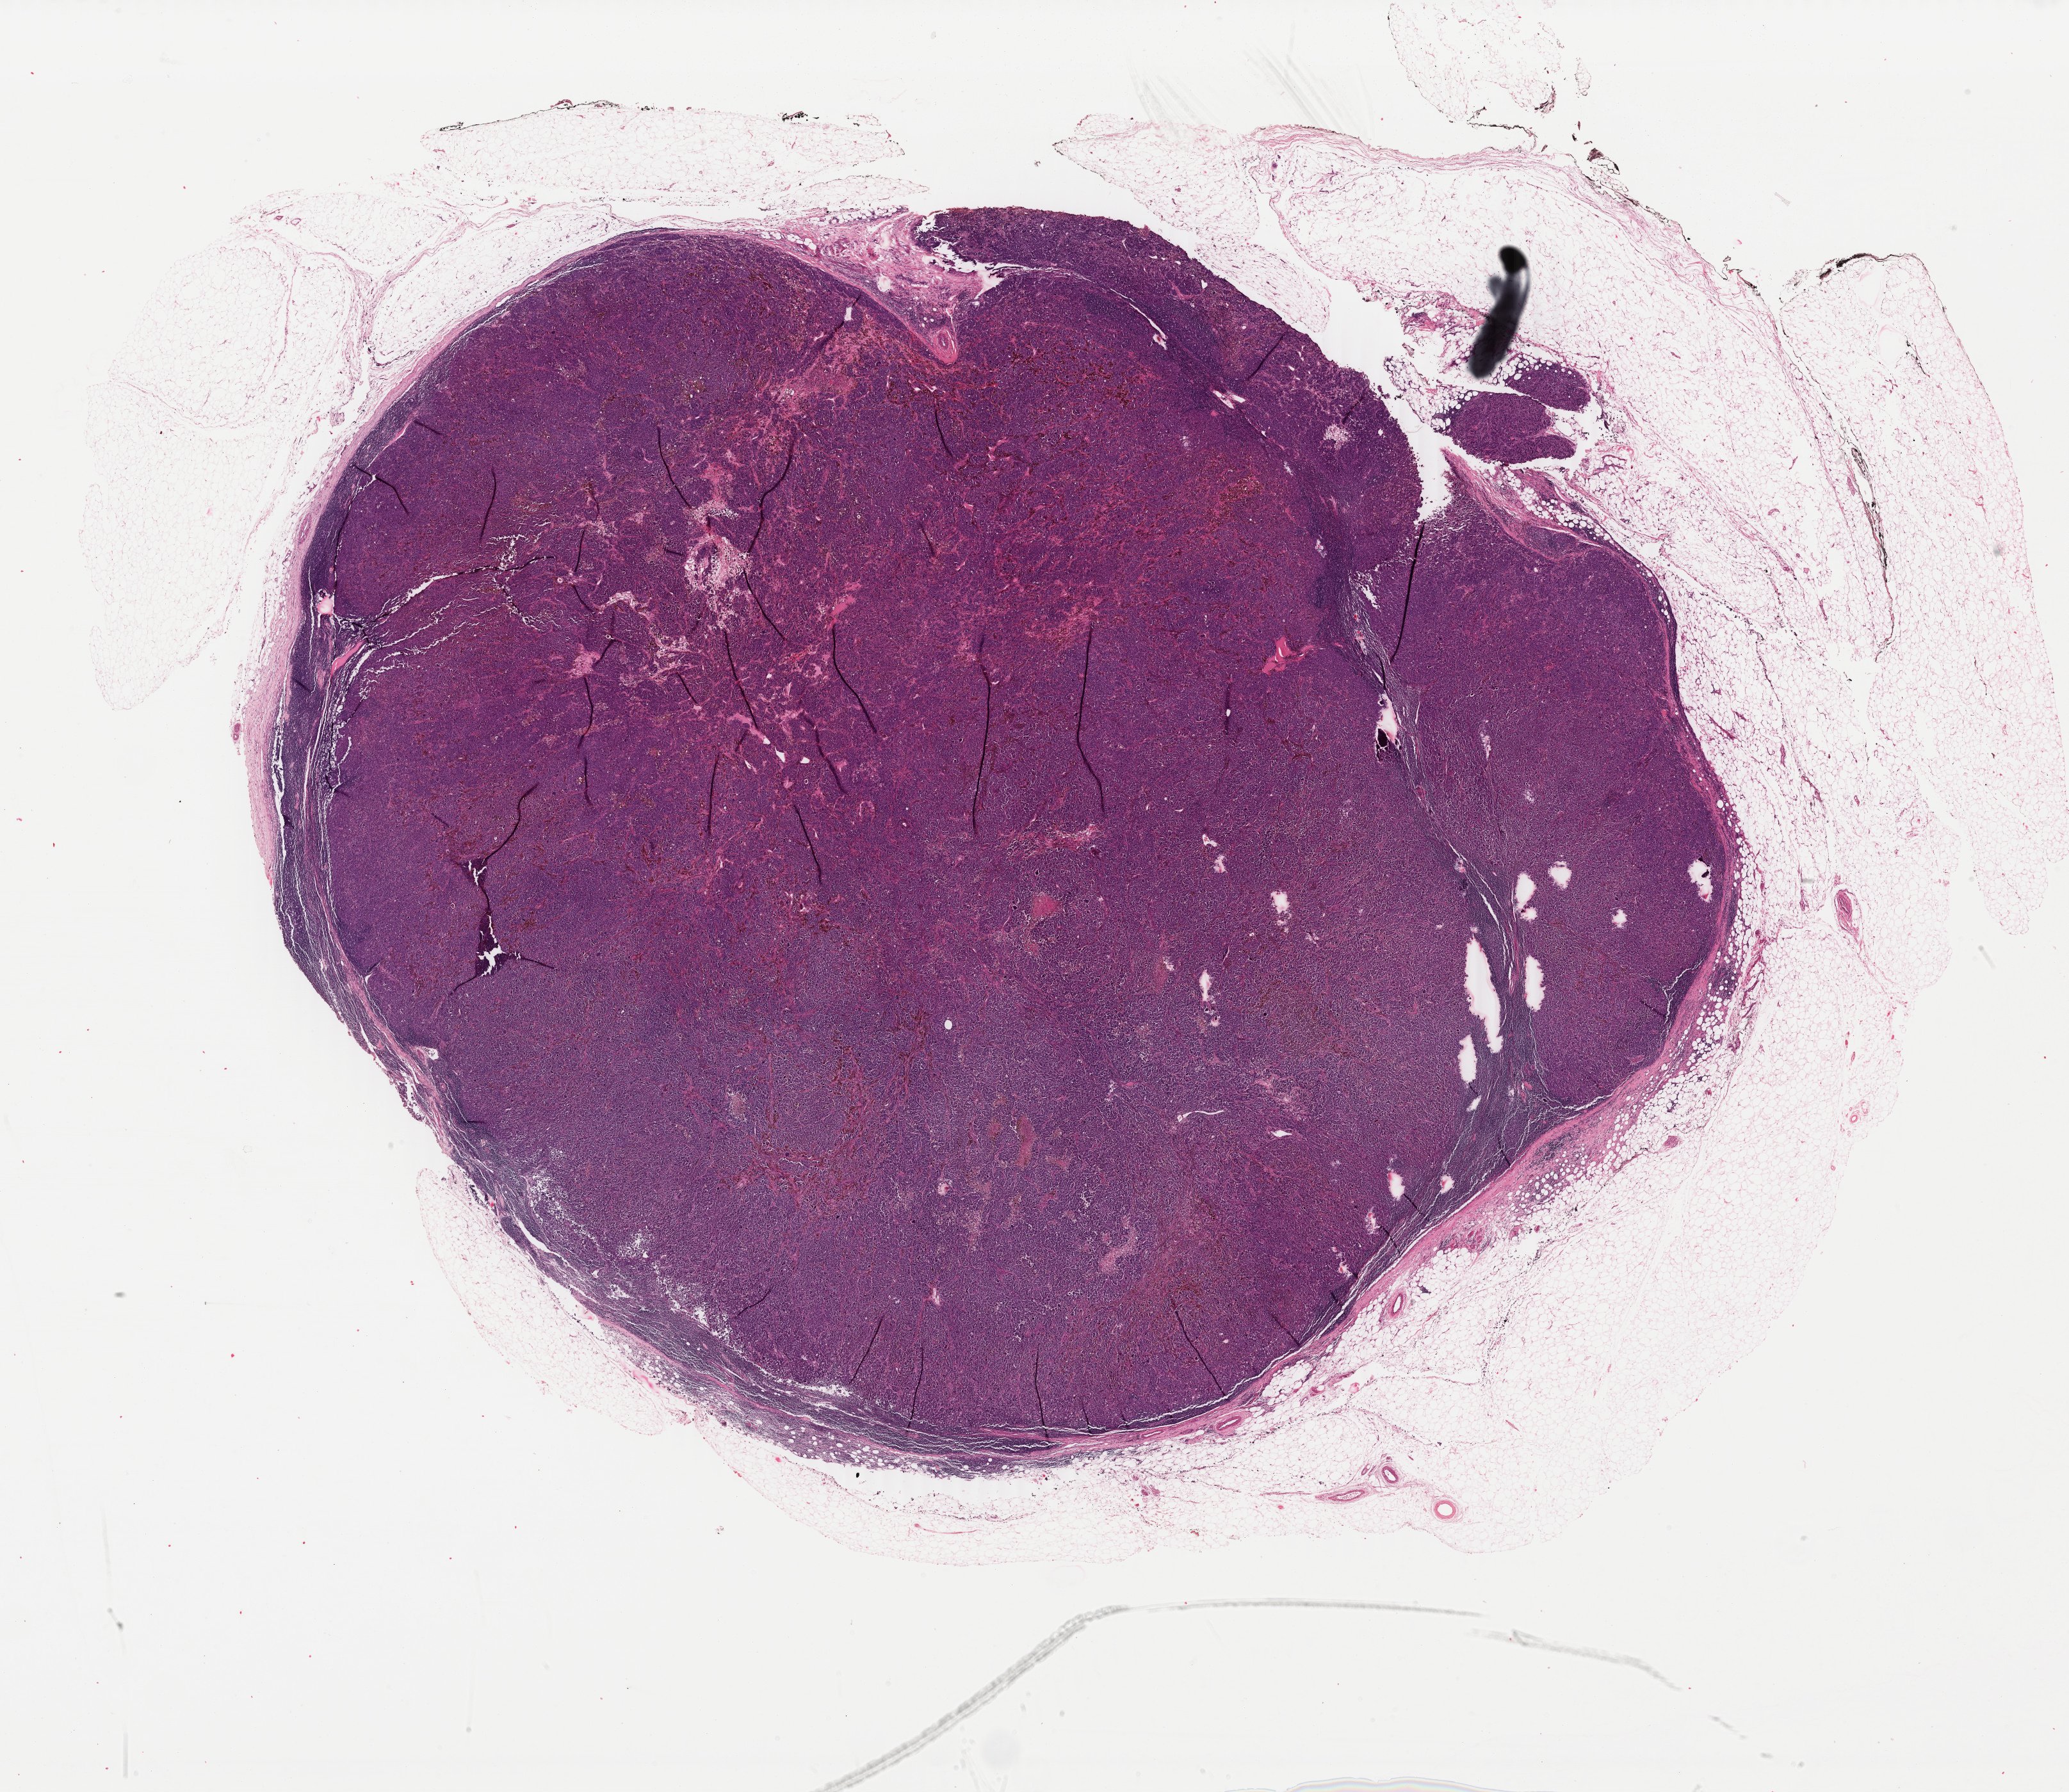
Whole-slide histology image, H&E, whole scanned area (about 25.7 x 22.3 mm, slide scanned at 40x) shown as a low-resolution overview; FFPE section; primary tumour sample from the skin. Male, age 71 years at initial diagnosis.
Pathologic diagnosis: Malignant melanoma, NOS.